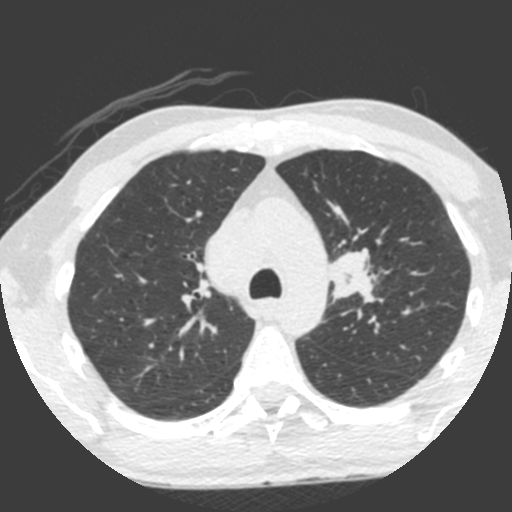
Low-dose screening chest CT, one axial slice. Position 154 of 212 along the scan axis. 120 kVp. Lung window (W 1500 / L -600 HU). 2 mm slice thickness. 512 × 512 image matrix.
Annotated regions visible in this slice (outlined manually by an expert reader):
- lesion 1 (tumor, upper lobe of left lung): bounding box [x1, y1, x2, y2] px = [328, 248, 375, 303]